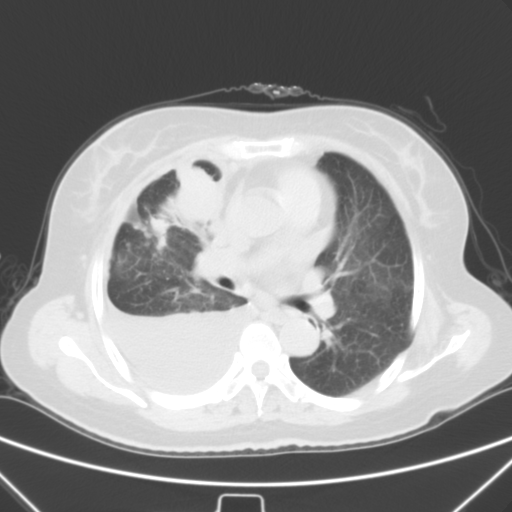
Chest CT, one axial slice; 120 kVp; lung window (W 1500 / L -600 HU); 5 mm slice thickness; 512 × 512 image matrix. Female patient, age 66 years. From the clinical record (not read from this slice): clinical TNM (as recorded): T2 N0 M1.
Structures marked on this image (bounding box drawn by a radiologist):
- lung tumour (recorded histology: adenocarcinoma): bounding box (x1, y1, x2, y2) in pixels: (169, 162, 220, 224)